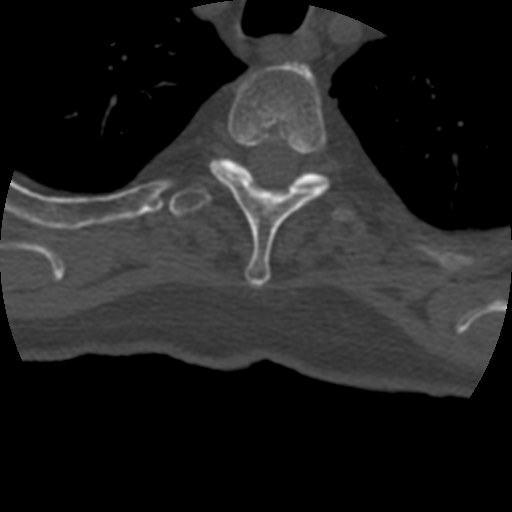
CT including the spine, one axial slice; bone window (W 1800 / L 400 HU); 512 × 512 image matrix, field of view 160 × 160 mm. Patient age 69 years. Case-level facts recorded for this patient, not image findings: primary cancer: prostate.
Structures marked on this image (semi-automatic segmentation, software-assisted and operator-edited):
- T3 vertebra: bounding box [x1, y1, x2, y2] px = [210, 63, 330, 287]
- T4 vertebra: [169, 158, 366, 235]